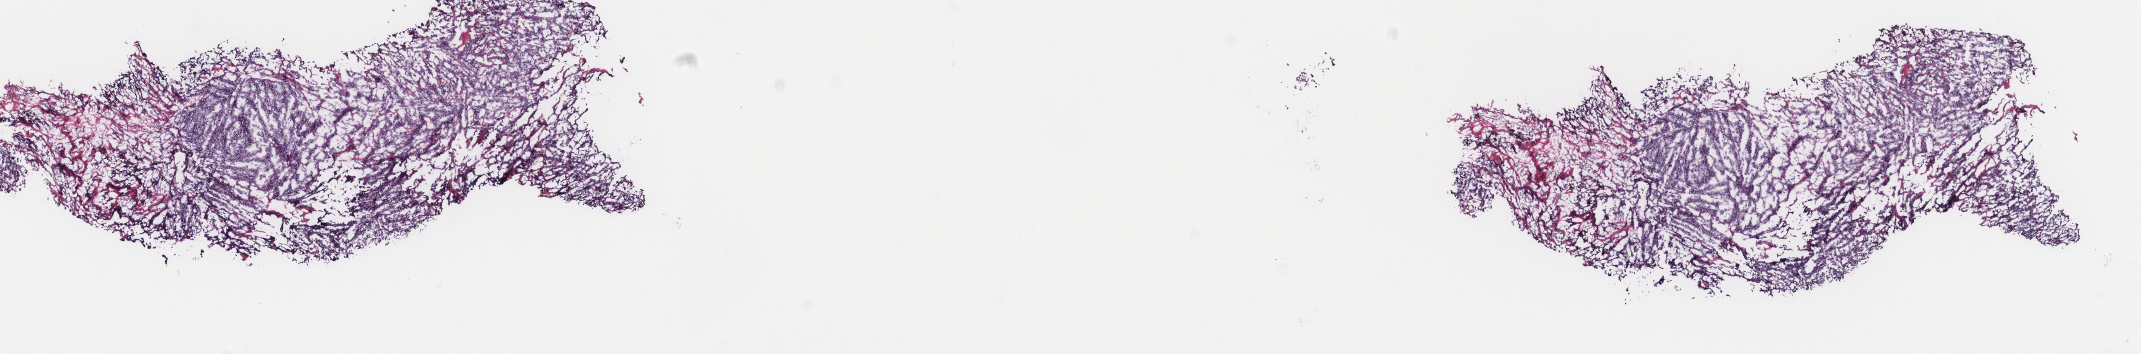
H&E-stained whole-slide image — a low-resolution overview of the entire scanned area, about 17.0 x 2.8 mm (from a 40x scan), frozen section, metastatic tumour sample, sampled site: skin. Female patient; age at initial diagnosis 27 years. Composition of this section per pathologist review: tumour cells 90%, tumour nuclei 85%, normal cells 0%, stromal cells 10%, necrosis 0%. Inflammatory infiltration, as recorded: lymphocyte infiltration 0%, monocyte infiltration 0%, neutrophil infiltration 0%.
This section: metastatic tumour tissue. Patient diagnosis: Malignant melanoma, NOS.